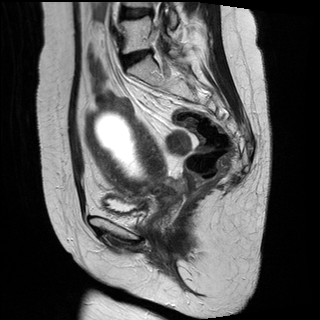
Pelvic MRI for cervical cancer, one sagittal slice. Slice 13 of 29 in the series (ordered by position). T2-weighted. 1.5 T. TE 89 ms, TR 2930 ms. 4 mm slice thickness. 320 × 320 image matrix. Female patient, age 49 years.
Outlined on this slice (outlined manually by an expert reader):
- uterus and cervix: bounding box (x1, y1, x2, y2) in pixels: (86, 104, 189, 215)